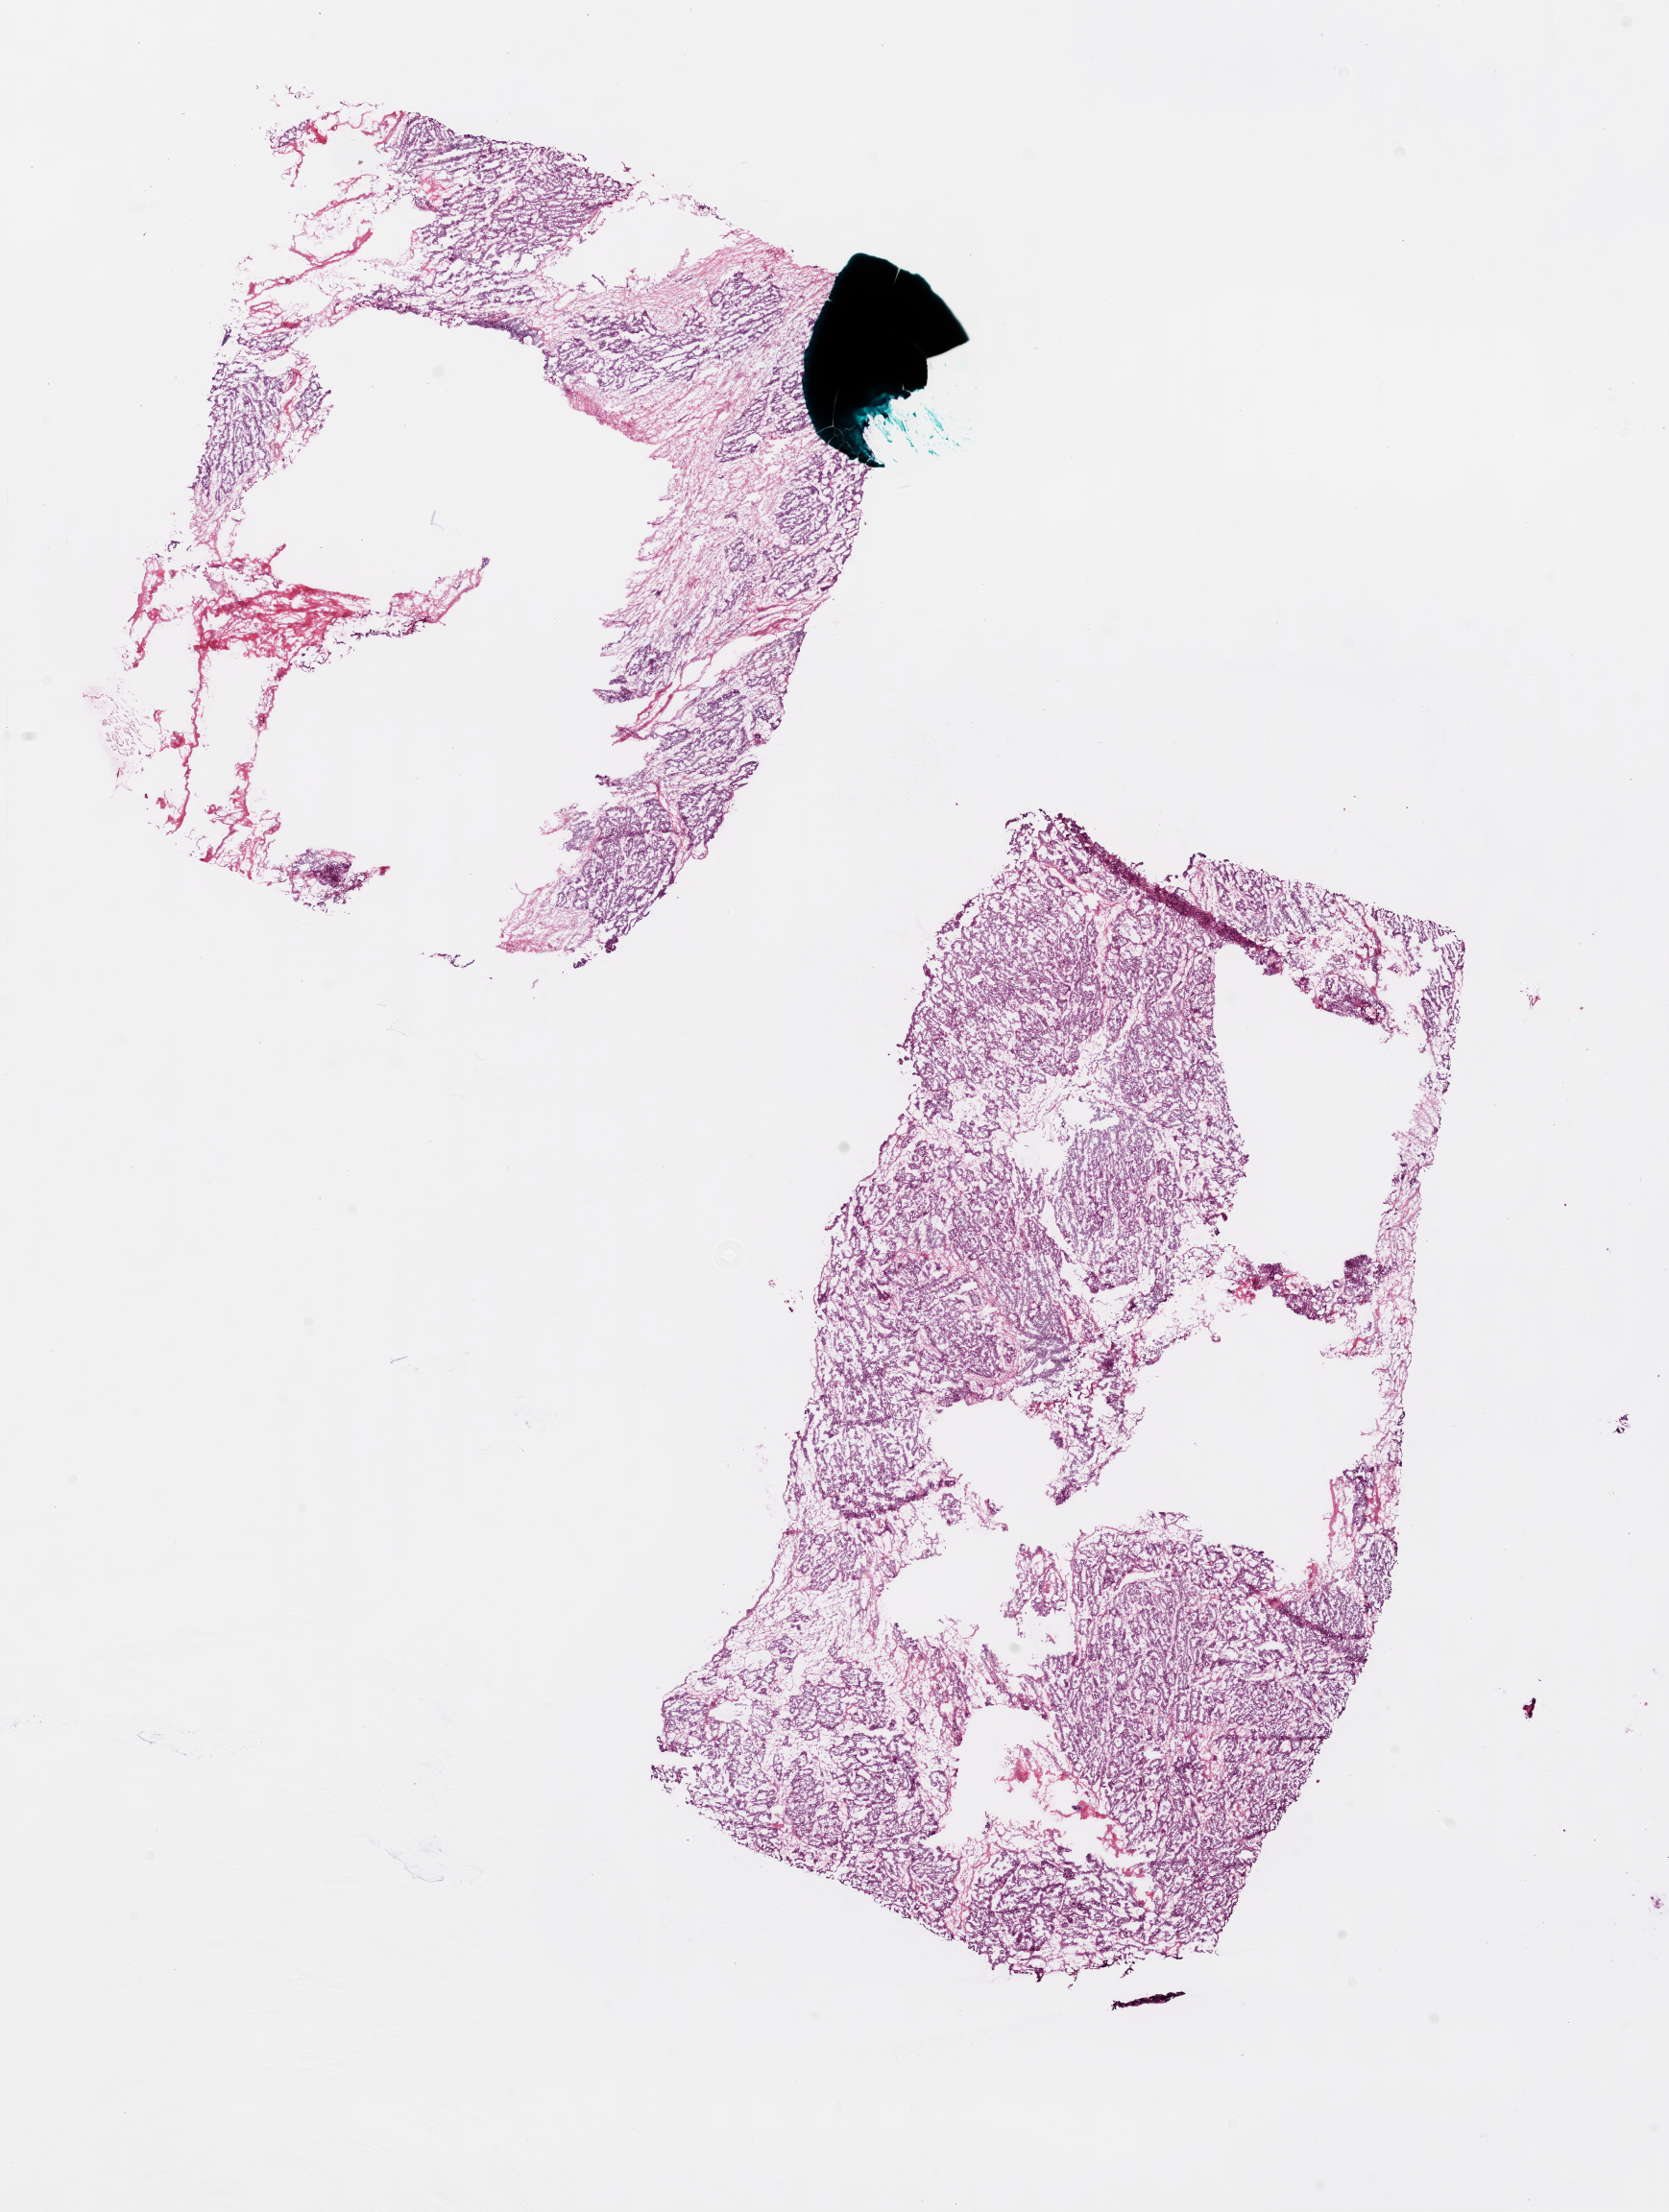
Whole-slide histology image, H&E, whole scanned area (about 14.0 x 18.6 mm) shown as a low-resolution overview. Frozen section. Ovary, primary tumour sample. Female, age 58 years at initial diagnosis. Histologic grade: G3 (poorly differentiated). Composition of this section per pathologist review: tumour cells 90%, tumour nuclei 95%, normal cells 0%, stromal cells 10%, necrosis 0%. Infiltration values recorded for this section: lymphocyte infiltration 90%.
Diagnosis: Serous cystadenocarcinoma, NOS. FIGO stage: IIIC.